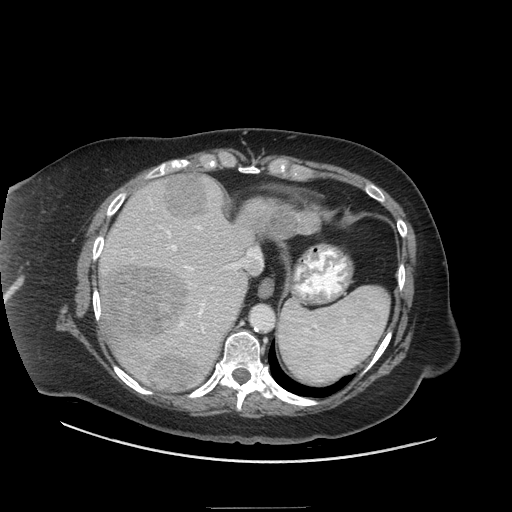
Contrast-enhanced abdominal CT (liver protocol), one axial slice; slice 51 of 81 in the series (ordered by position); soft-tissue window (W 400 / L 40 HU); 2.5 mm slice thickness; 512 × 512 image matrix, field of view 440 × 440 mm. Case-level facts recorded for this patient, not image findings: diagnosis: hepatocellular carcinoma (patient treated with transarterial chemoembolisation; whether this scan precedes or follows treatment is not stated here); TNM stage (as recorded): Stage-II; Child-Pugh class: A; tumour differentiation: moderately differentiated.
Annotated regions visible in this slice (semi-automatically segmented with operator editing):
- liver parenchyma outside the tumour (the mass and vessels are separate outlines, so this box may not span the whole liver): bounding box (x1, y1, x2, y2) in pixels: (98, 176, 268, 390)
- mass: (104, 174, 318, 392)
- liver vessels: (104, 196, 263, 345)